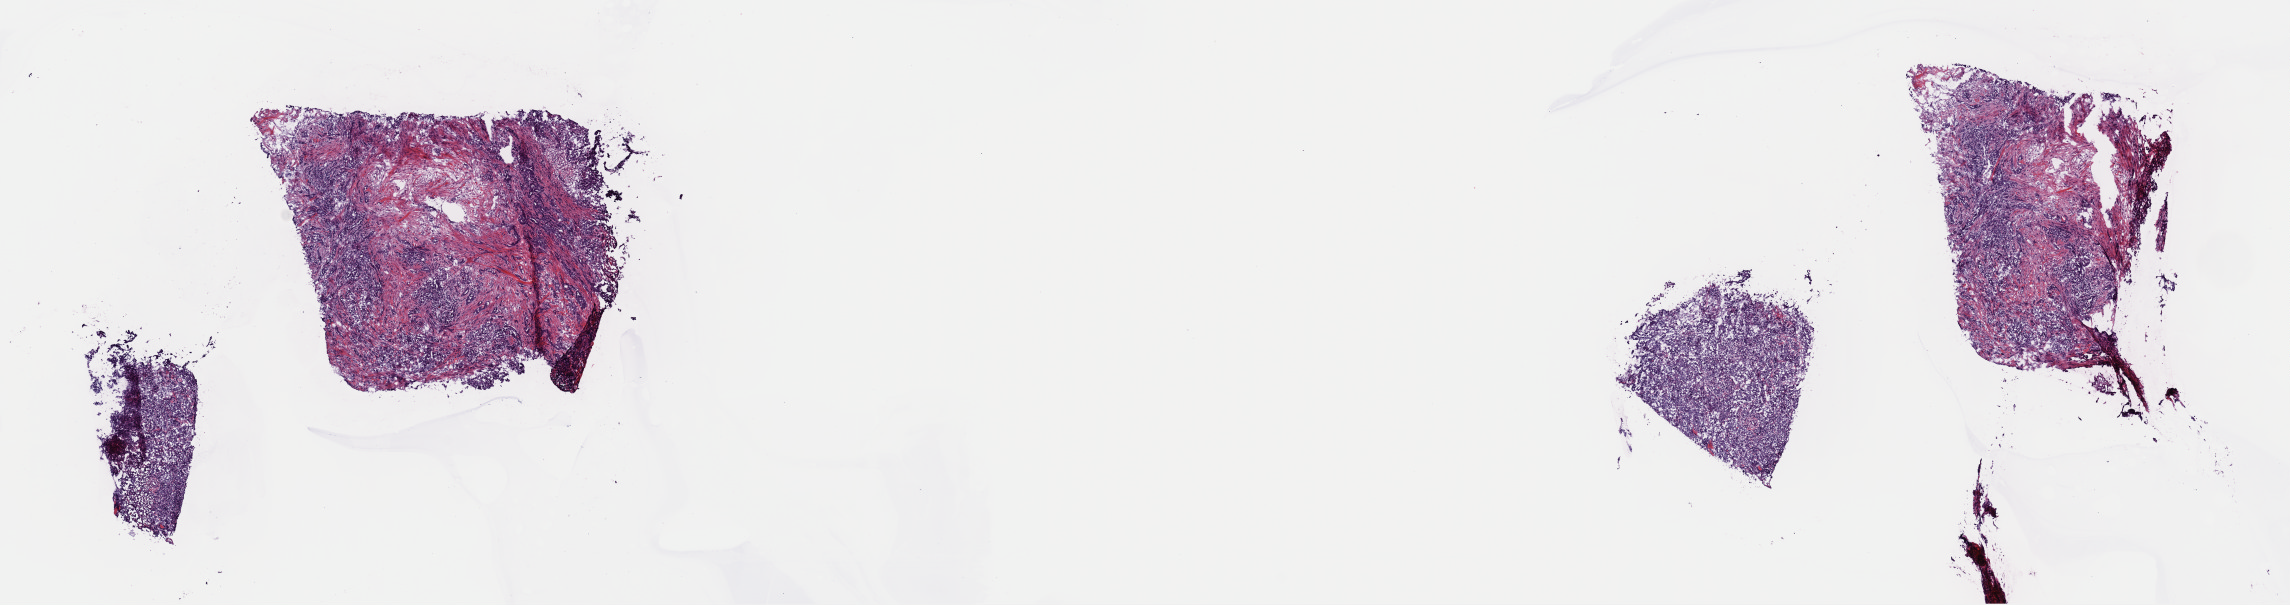
Digitized Hematoxylin and eosin (H&E) stained tissue section (whole slide), a low-resolution overview of the entire scanned area, about 18.1 x 4.8 mm (acquisition: 40x scan), frozen section from the top of the tissue portion, breast, primary tumour sample. Patient: female, age at initial diagnosis 48 years. Composition of this section per pathologist review: tumour cells 55%, tumour nuclei 90%, normal cells 0%, stromal cells 44%, necrosis 1%. Inflammatory infiltration, as recorded: lymphocyte infiltration 5%, monocyte infiltration 0%, neutrophil infiltration 0%.
Lymph nodes positive (case pathology): 2 of 14 examined. Histologic diagnosis: Infiltrating duct carcinoma, NOS. AJCC pathologic stage: IIB.